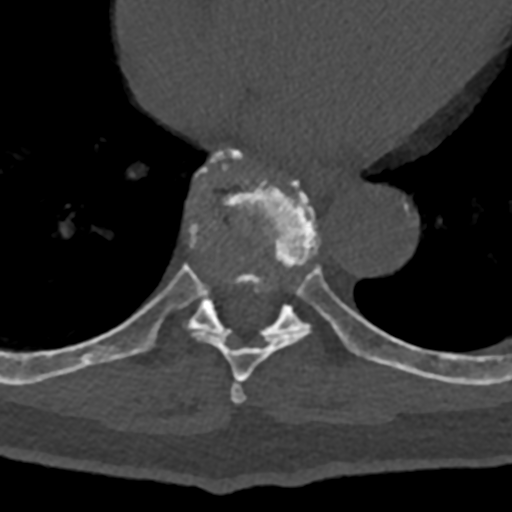
CT including the spine, one axial slice; slice 685 of 797 in the series (ordered by position); reconstruction kernel Br40s/3; 120 kVp; bone window (W 1800 / L 400 HU); 0.5 mm slice thickness; 512 × 512 image matrix, field of view 160 × 160 mm. Male patient, age 74 years. Case-level facts recorded for this patient, not image findings: primary cancer: renal; vertebrae with lytic lesions (as recorded): T10, L1, L2, L3, L4, L5.
Structures marked on this image (semi-automatic segmentation, software-assisted and operator-edited):
- T7 vertebra: box from (x=230, y=380) to (x=247, y=404) px
- T8 vertebra: (x=70, y=152)–(x=365, y=382)
- T9 vertebra: (x=88, y=149)–(x=432, y=379)